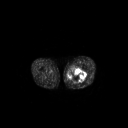
FDG PET of an extremity soft-tissue mass (from a PET/CT study), one axial slice. Position 241 of 267 along the scan axis. 3.27 mm slice thickness. 128 × 128 image matrix, field of view 700 × 700 mm. Patient: male, 44 years. From the clinical record (not read from this slice): histological type: undifferentiated pleomorphic liposarcoma; grade: high; site of the primary tumour: left thigh.
Outlined on this slice (expert contour drawn on MRI and transferred to this co-registered scan by the dataset authors):
- gross tumour volume including surrounding oedema: bounding box <67,68,86,83> (left, top, right, bottom; pixels)
- gross tumour volume (mass): <67,68,86,82>